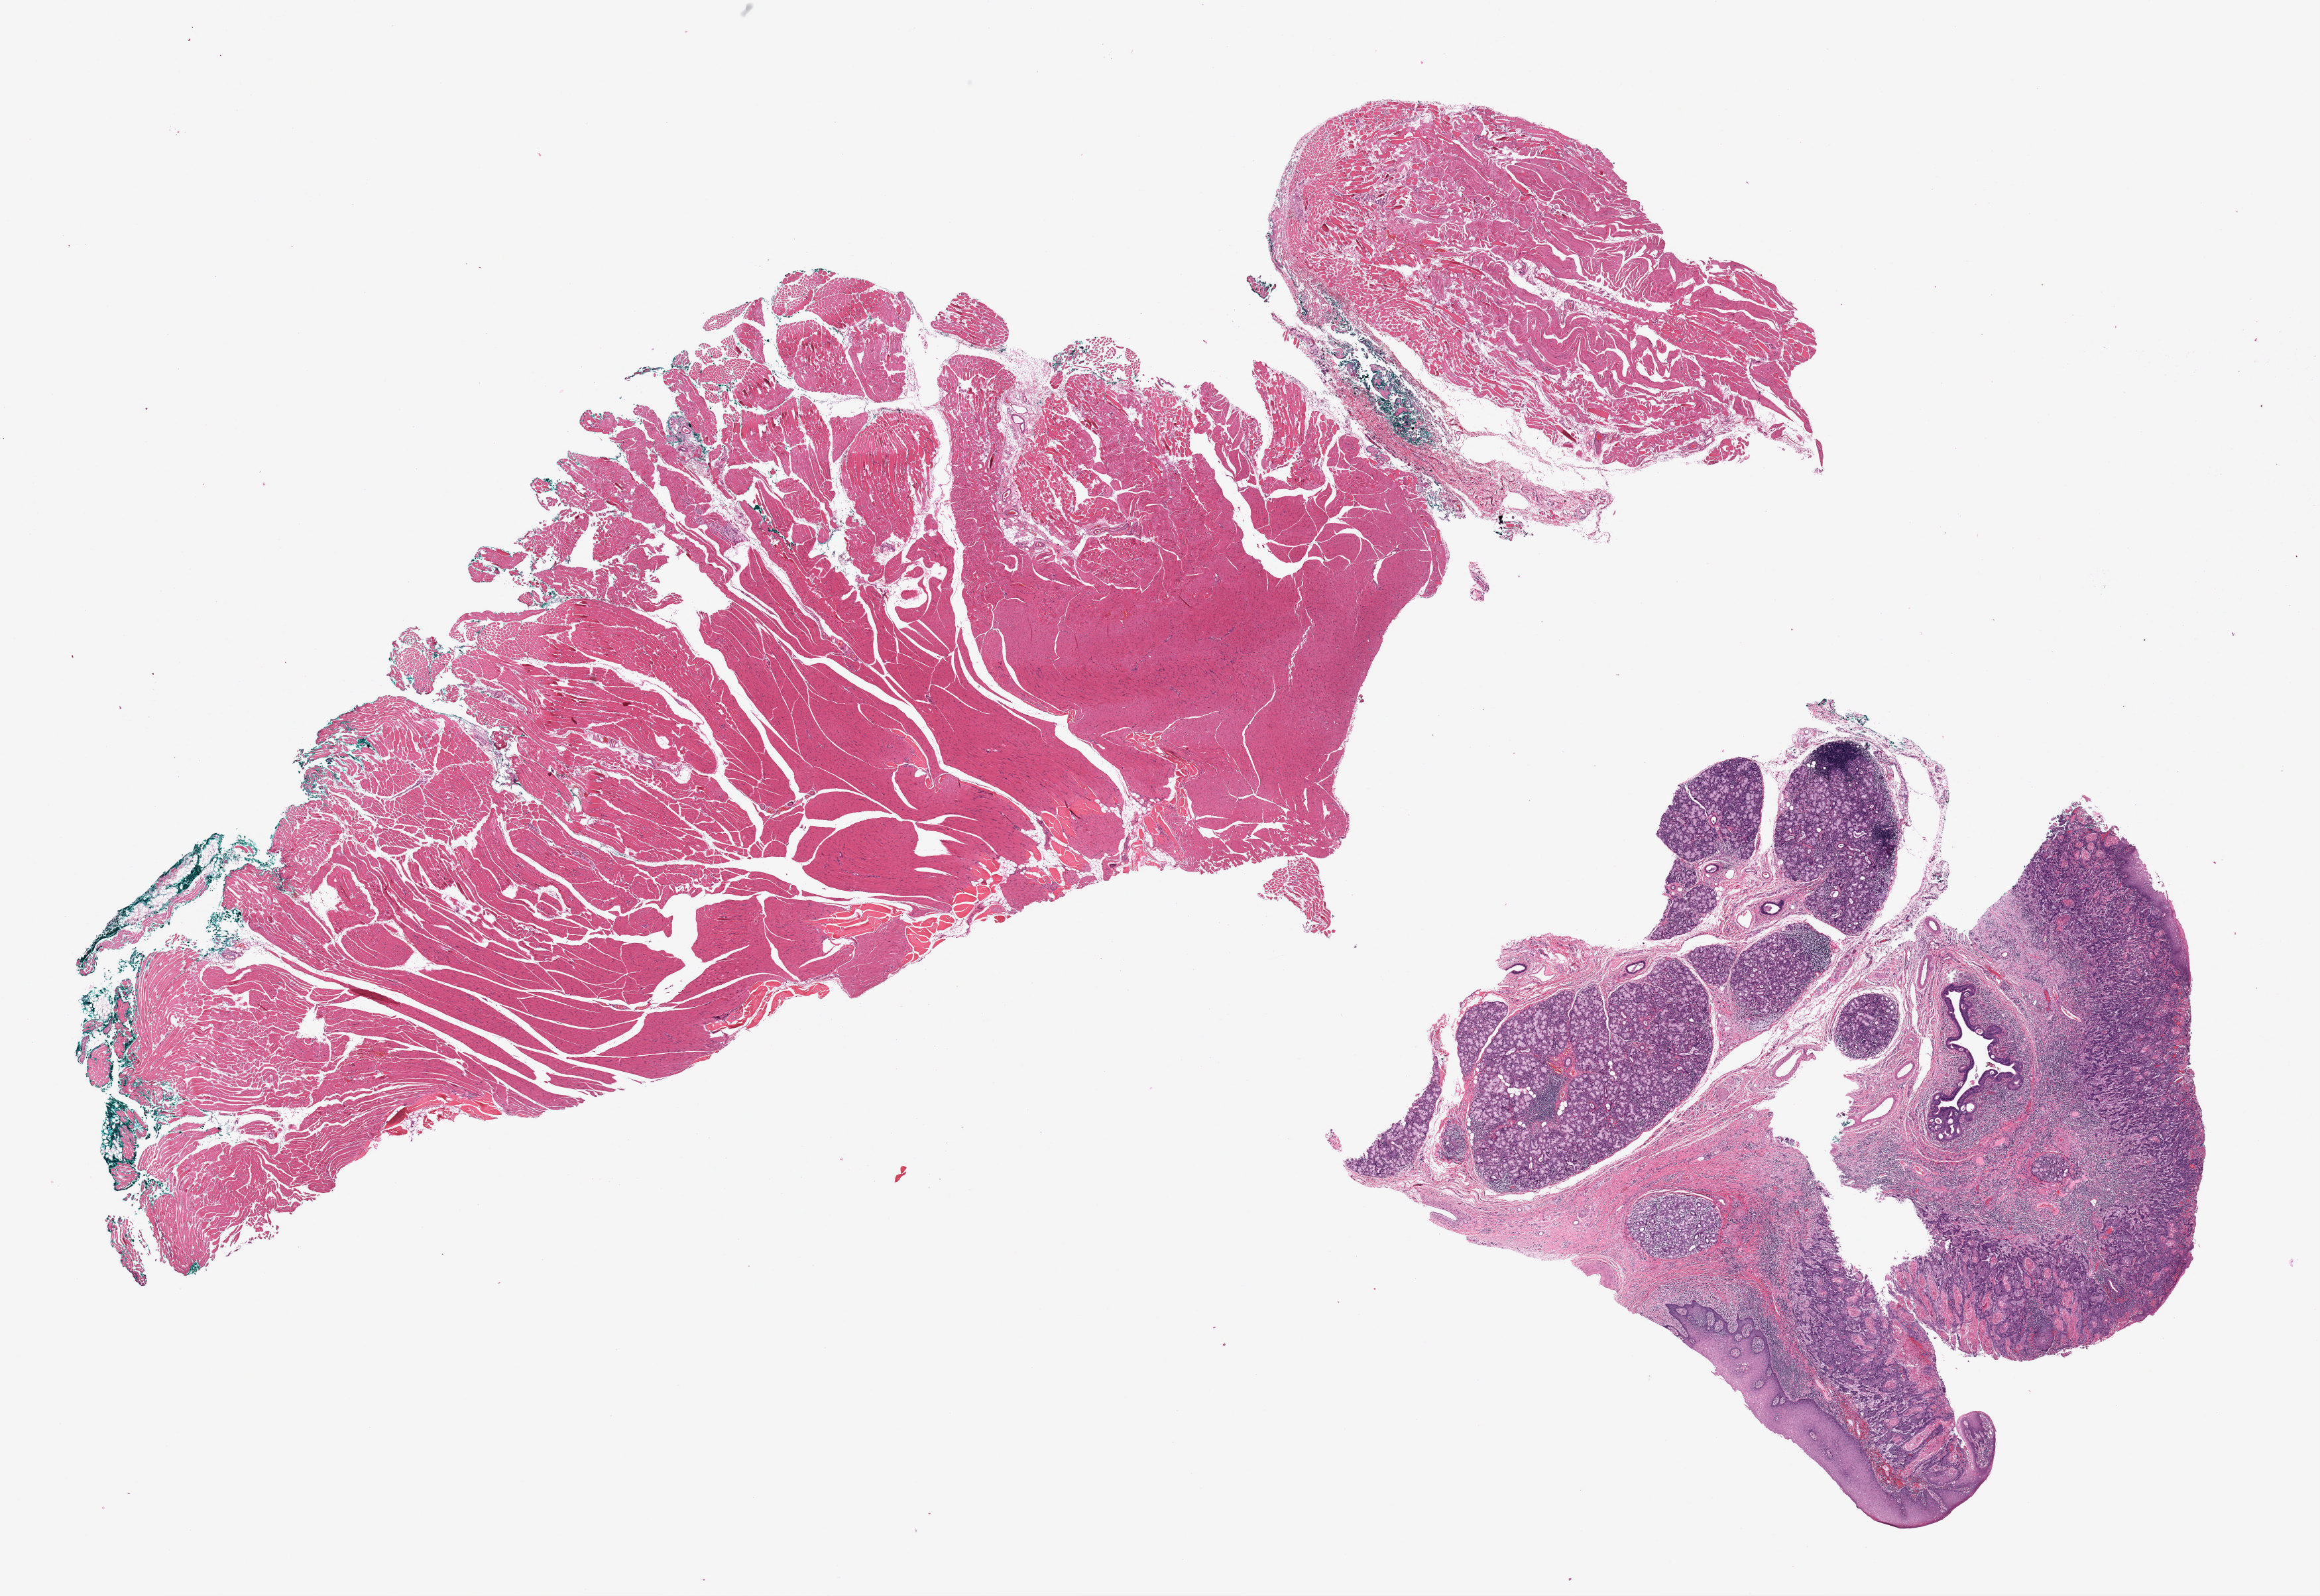
Digitized H&E tissue section (whole slide), low-resolution overview of the scanned area, about 27.9 x 19.2 mm, formalin-fixed paraffin-embedded (FFPE) diagnostic section, head and neck, primary tumour sample. Male patient; age at initial diagnosis 55 years. Histologic grade: G2 (moderately differentiated).
AJCC pathologic stage: II (7th edition). Diagnosis: Squamous cell carcinoma, keratinizing, NOS (anterior floor of mouth).